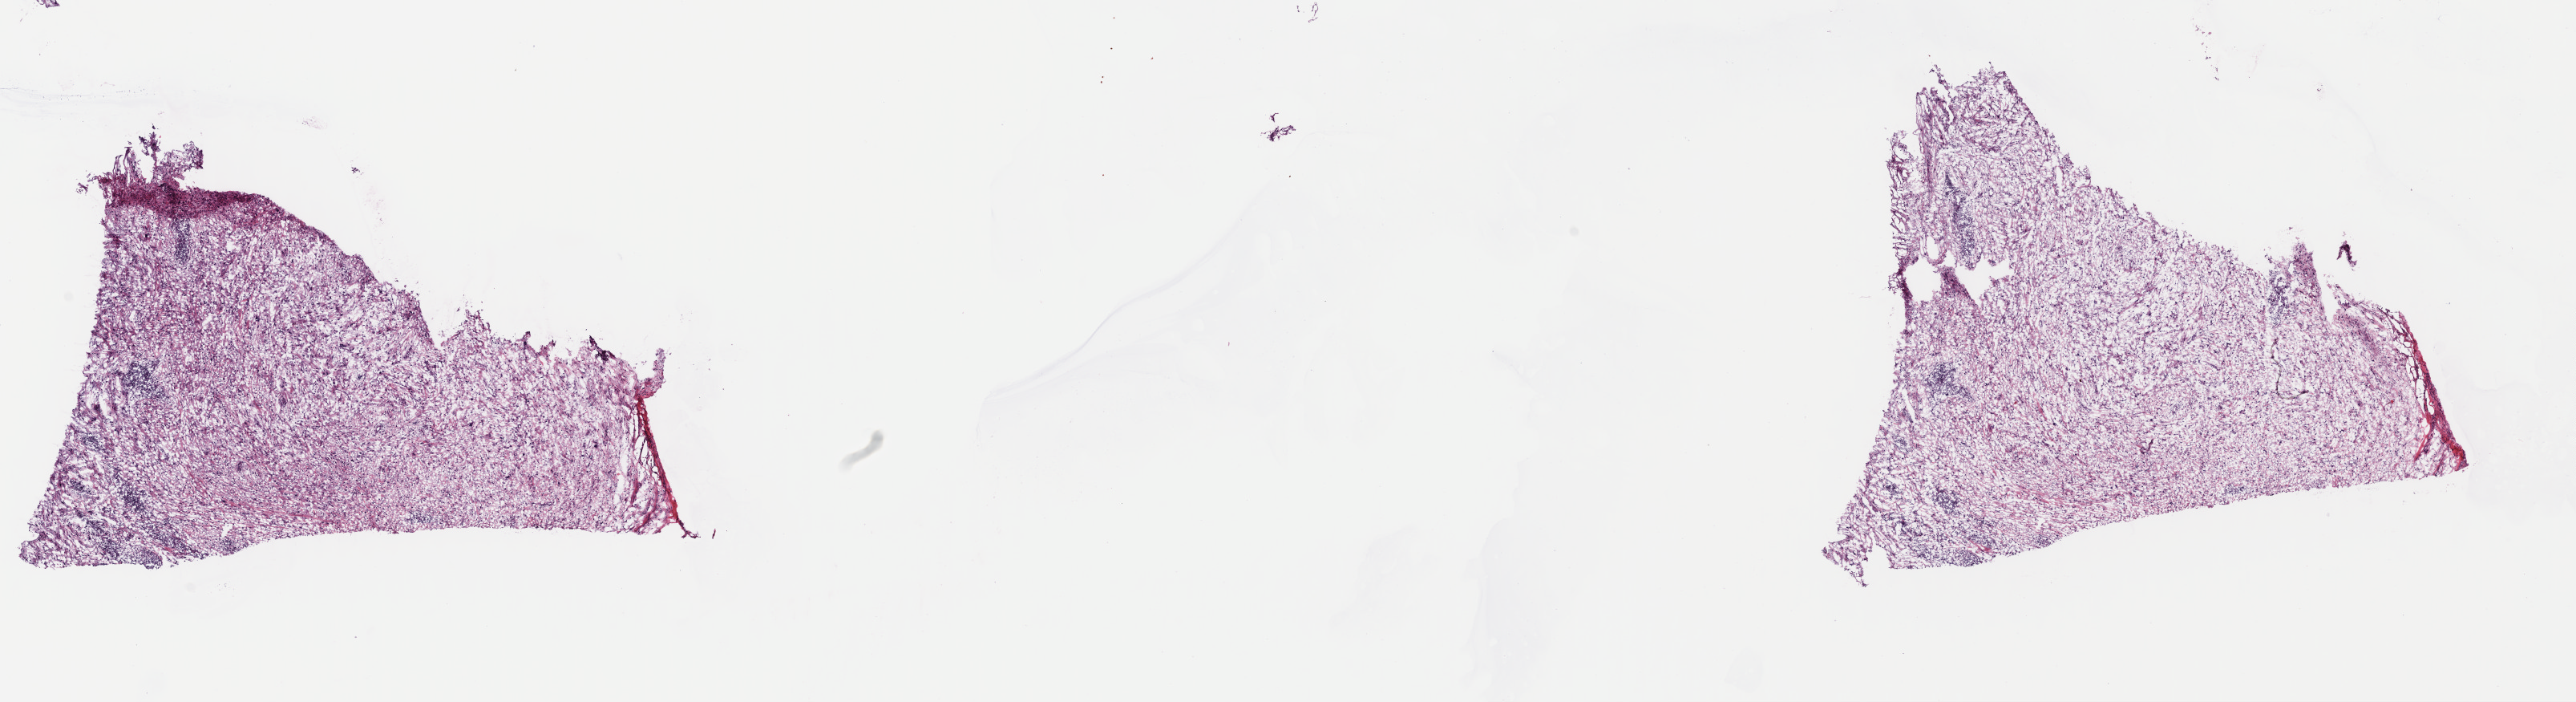
Whole-slide histology image, H&E — low-resolution overview of the scanned area, about 25.3 x 6.9 mm, frozen section from the top of the tissue portion, connective, subcutaneous and other soft tissues, primary tumour sample. Patient: female, age at initial diagnosis 78 years. Pathologist review of this section (percent, as recorded): tumour cells 70%, tumour nuclei 70%, normal cells 0%, stromal cells 30%, necrosis 0%. Infiltration values recorded for this section: lymphocyte infiltration 3%, monocyte infiltration 2%, neutrophil infiltration 1%.
Diagnosis: Fibromyxosarcoma (connective, subcutaneous and other soft tissues of lower limb and hip).